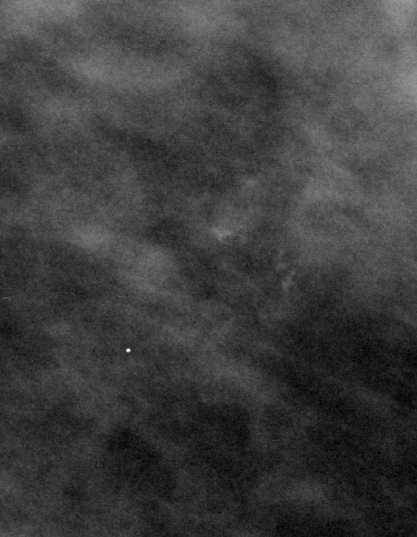
Cropped region of a digitized screen-film mammogram centred on a radiologist-marked abnormality; left breast; MLO view.
Finding: calcifications, morphology pleomorphic, distribution clustered; BI-RADS assessment category 4; subtlety rating 3 on a 1 (subtle) to 5 (obvious) scale; pathology result (as recorded, not read from the image): benign.